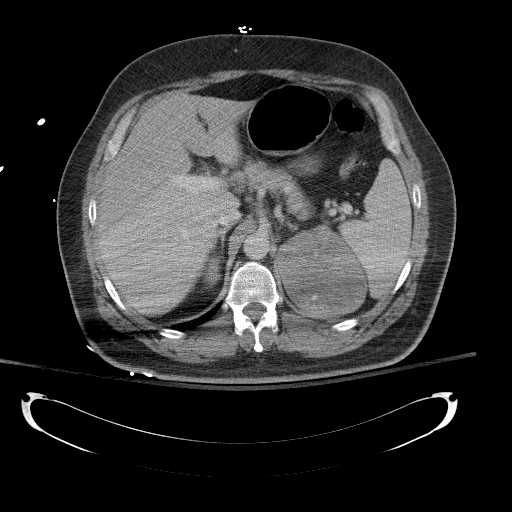
Contrast-enhanced abdominal CT, one axial slice. Slice 90 of 154 in the series (ordered by position). Reconstruction kernel B41f. 120 kVp. Intravenous contrast given. Soft-tissue window (W 400 / L 40 HU). 512 × 512 image matrix, field of view 467 × 467 mm. Patient: male, 43 years. From the clinical record (not read from this slice): diagnosis: adrenocortical carcinoma; tumour side: left adrenal.
Structures marked on this image (semi-automatic segmentation, software-assisted and operator-edited):
- mass: bounding box (x1, y1, x2, y2) in pixels: (279, 225, 366, 316)